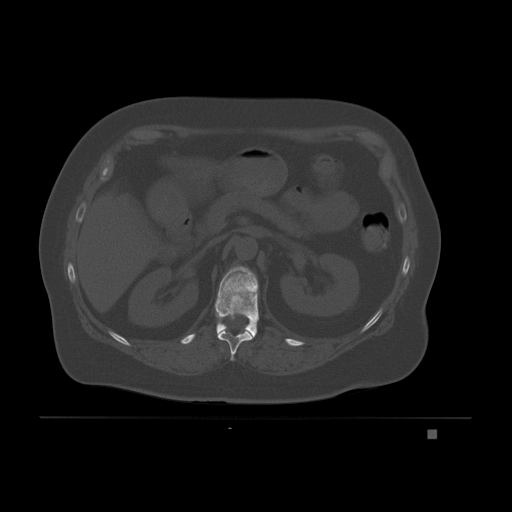
CT including the spine, one axial slice; position 84 of 221 along the scan axis; bone window (W 1800 / L 400 HU); 3 mm slice thickness; 512 × 512 image matrix, field of view 474 × 474 mm. Patient: female, 63 years. Case-level facts recorded for this patient, not image findings: primary cancer: breast.
Outlined on this slice (semi-automatic segmentation, software-assisted and operator-edited):
- T11 vertebra: bounding box <217,330,252,361> (left, top, right, bottom; pixels)
- T12 vertebra: <214,266,259,338>